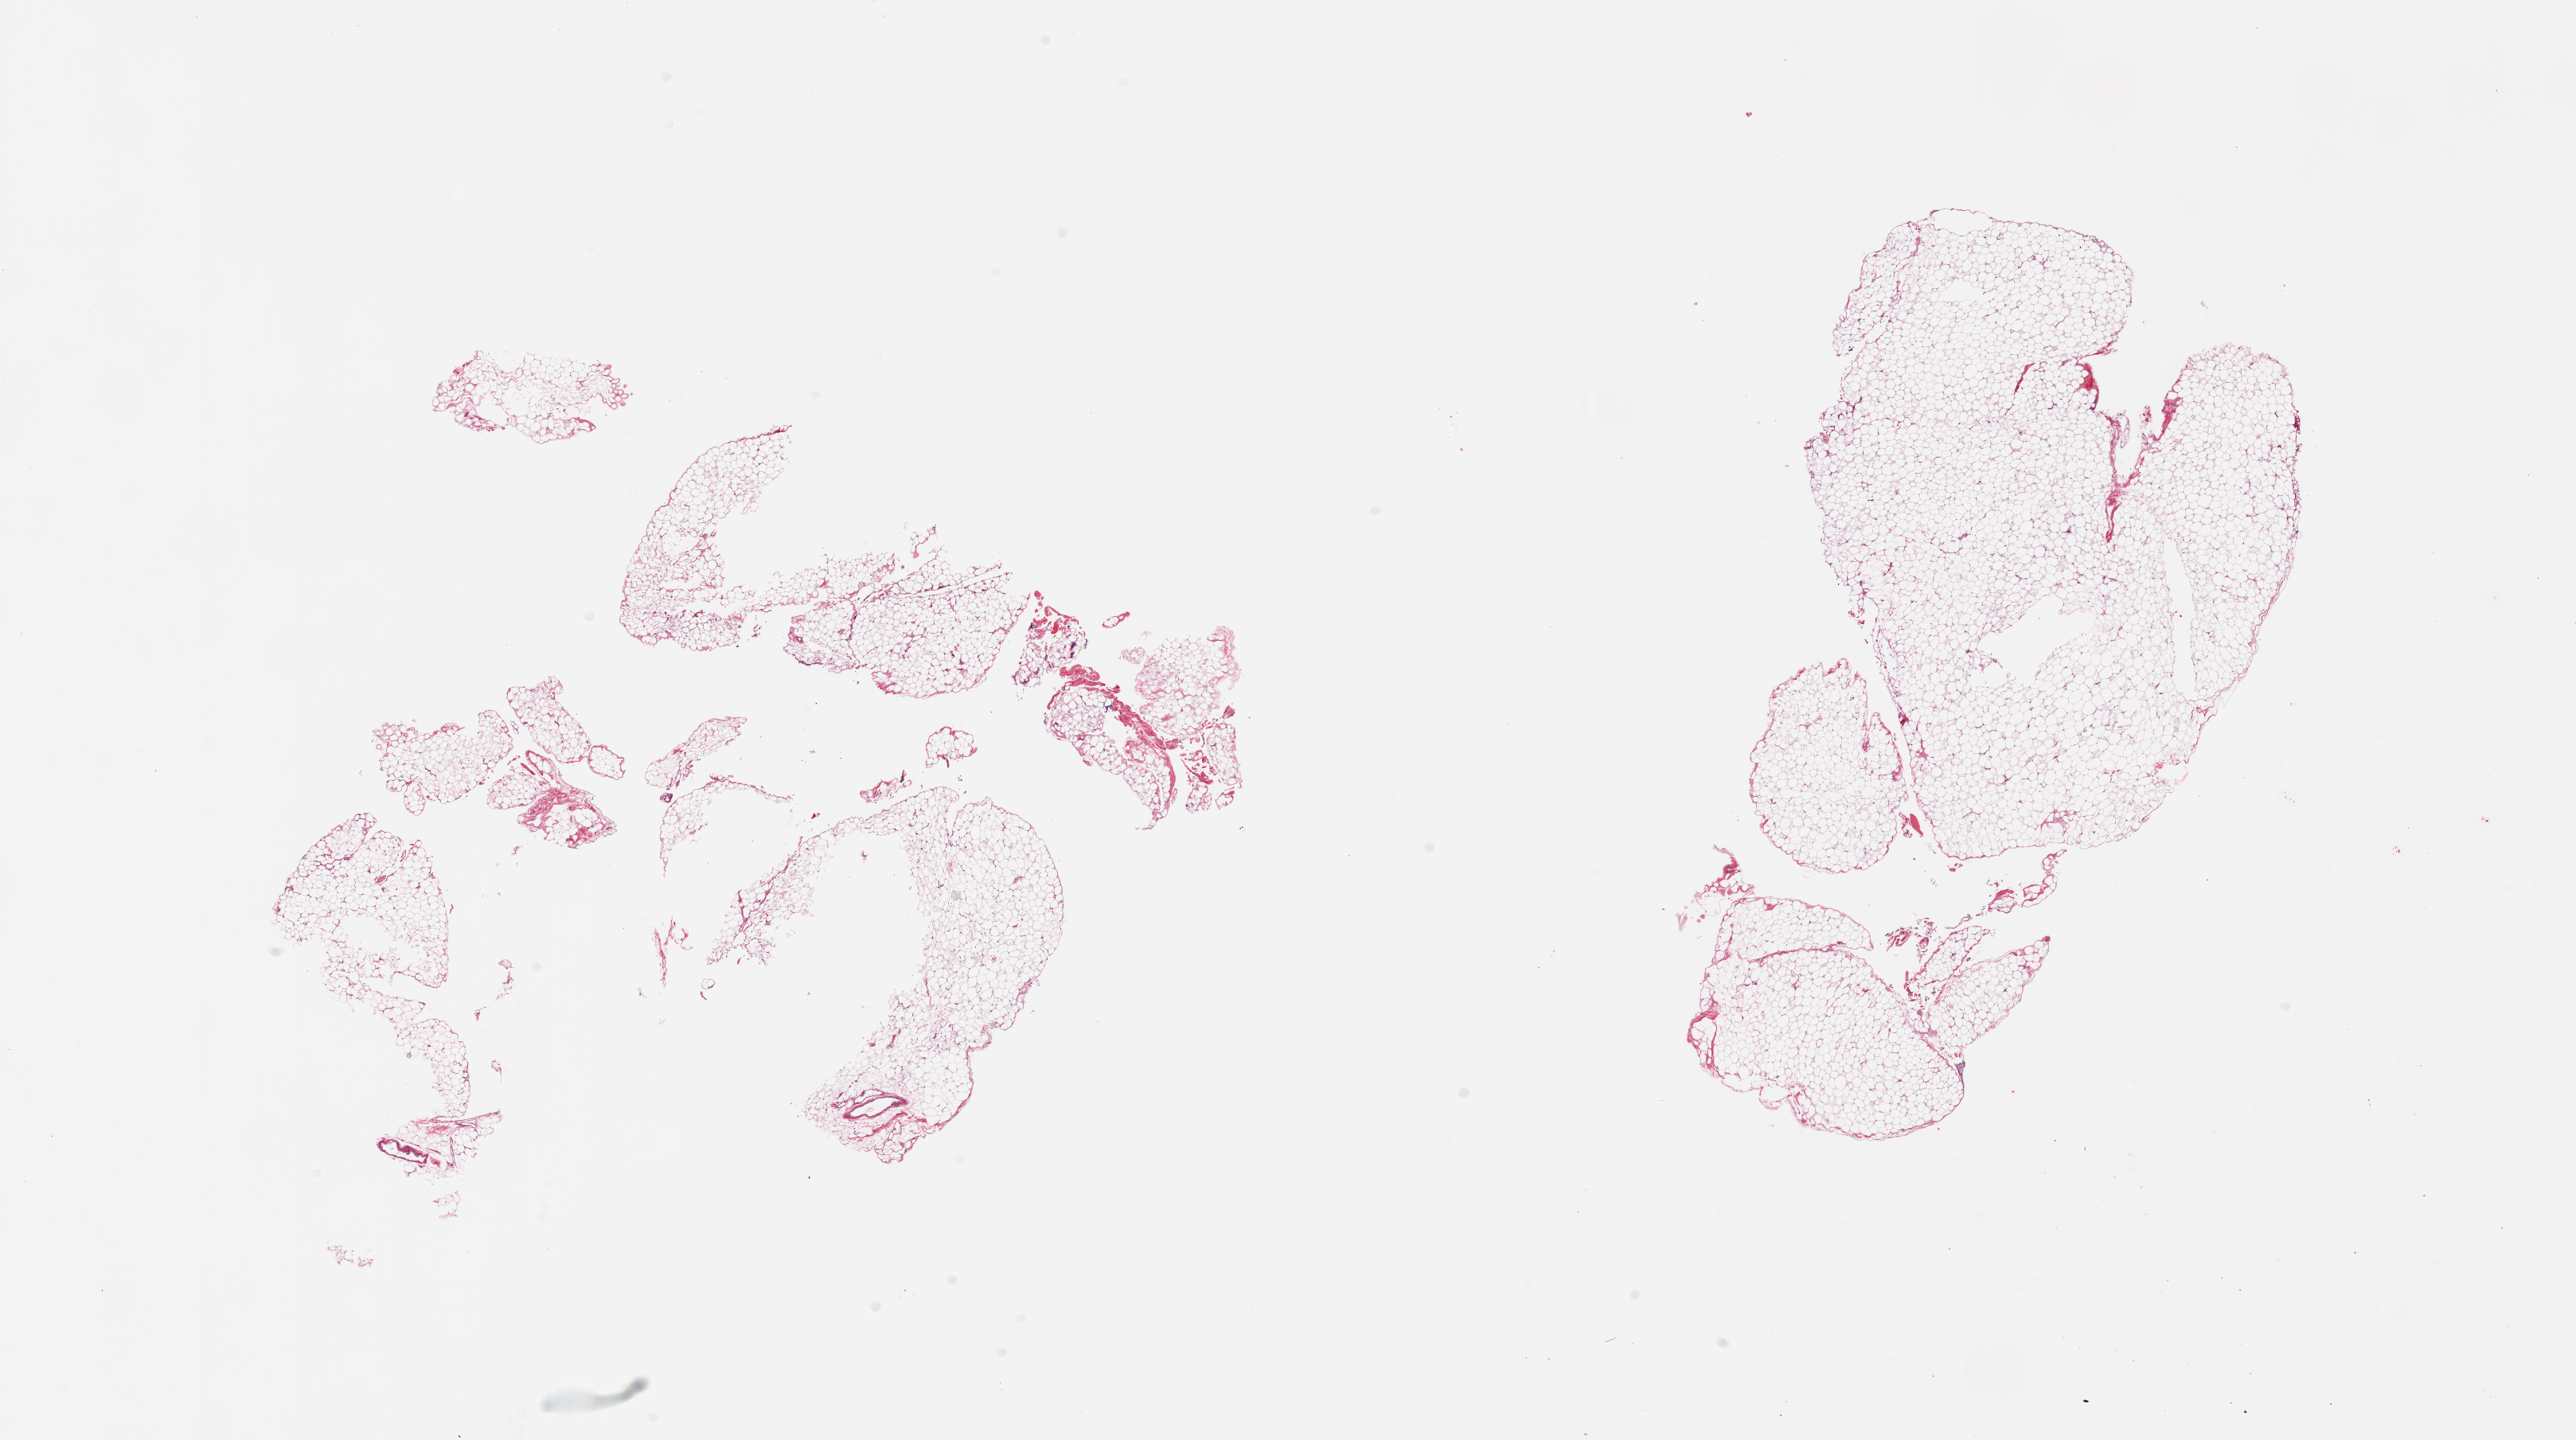
Digitized H&E-stained section — whole scanned area (about 25.6 x 14.3 mm) shown as a low-resolution overview, PAXgene-fixed, paraffin-embedded tissue, target tissue: omentum, donor tissue sample. Donor sex: male.
* pathologist's review note for this sample: 2 pieces; incomplete section (?poor fixation)